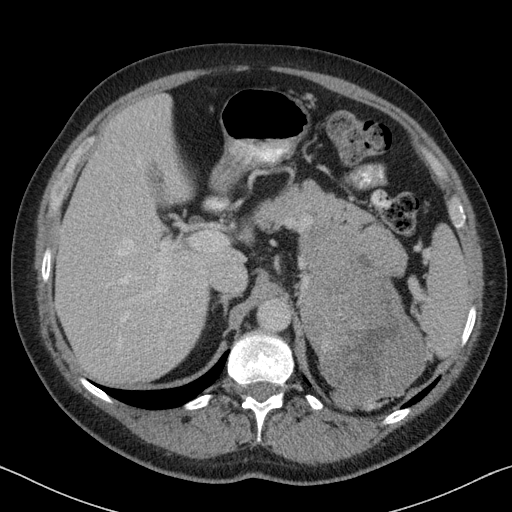
Contrast-enhanced abdominal CT, one axial slice; position 55 of 88 along the scan axis; reconstruction kernel B31f; intravenous contrast given; soft-tissue window (W 400 / L 40 HU); 512 × 512 image matrix, field of view 366 × 366 mm. Patient: male, 51 years. From the clinical record (not read from this slice): diagnosis: adrenocortical carcinoma; tumour side: left adrenal; tumour size at pathology: 16.5 cm; Ki-67 index: 30 %; stage (as recorded): 2.
Structures marked on this image (semi-automatic segmentation, software-assisted and operator-edited):
- mass: bounding box (x1, y1, x2, y2) in pixels: (302, 227, 425, 409)